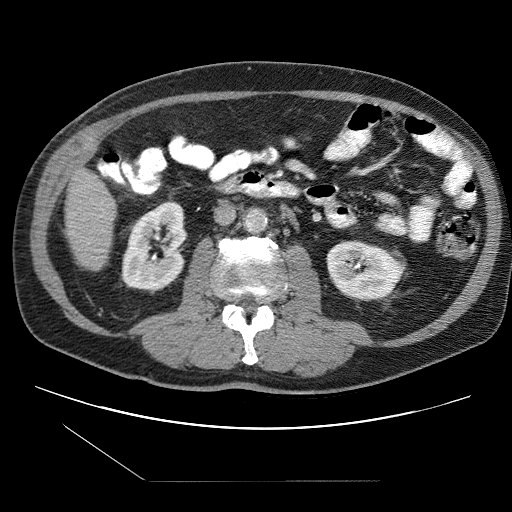
Contrast-enhanced abdominal CT (liver protocol), one axial slice; position 17 of 109 along the scan axis; 120 kVp; one of 2 acquisitions stored at this slice position; soft-tissue window (W 400 / L 40 HU); 2.5 mm slice thickness; 512 × 512 image matrix. Case-level facts recorded for this patient, not image findings: diagnosis: hepatocellular carcinoma (patient treated with transarterial chemoembolisation; whether this scan precedes or follows treatment is not stated here); TNM stage (as recorded): Stage-IIIB; Child-Pugh class: A; tumour differentiation: well differentiated.
Outlined on this slice (semi-automatically segmented with operator editing):
- liver parenchyma outside the tumour (the mass and vessels are separate outlines, so this box may not span the whole liver): bounding box (x1, y1, x2, y2) in pixels: (66, 168, 116, 268)